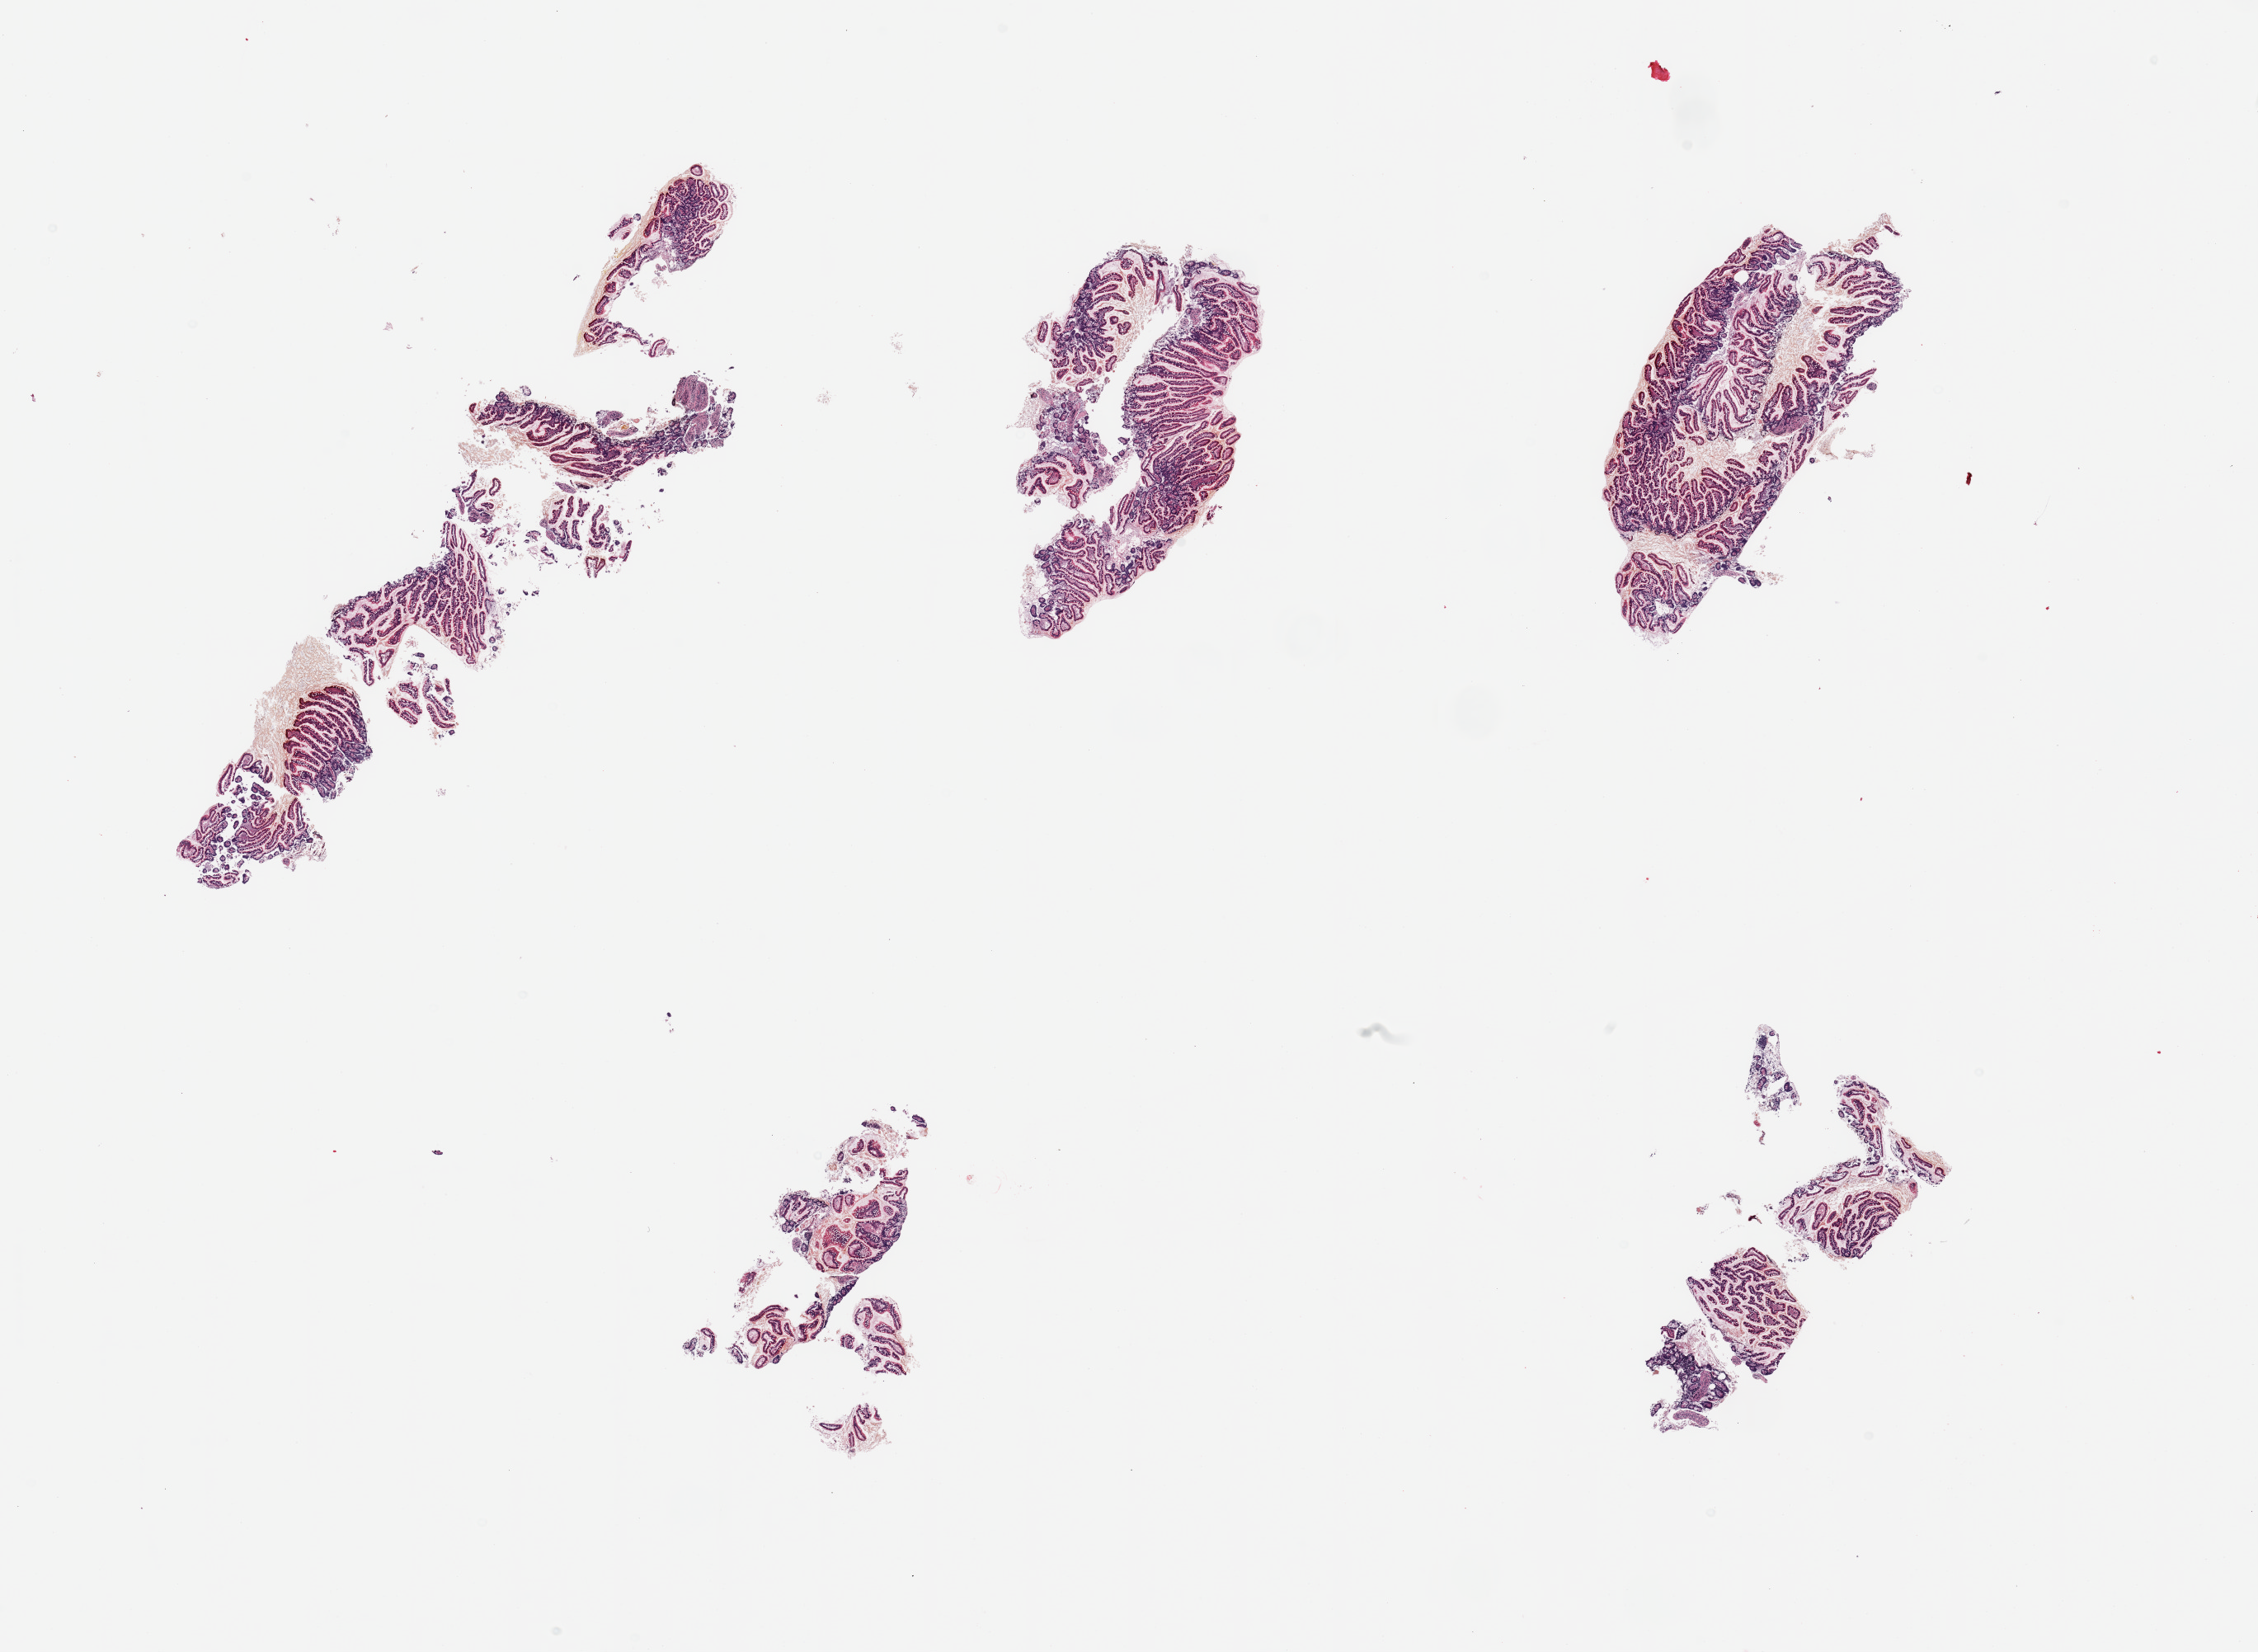
Digitized haematoxylin and eosin-stained section — shown as a low-resolution overview of the whole scanned area (about 21.7 x 15.8 mm, from a 20x scan); PAXgene-fixed, paraffin-embedded tissue; sampled site (target tissue): ileum; donor tissue sample.
- review note (as recorded): 5 pieces; preserved mucosa but no lymphoid nodules